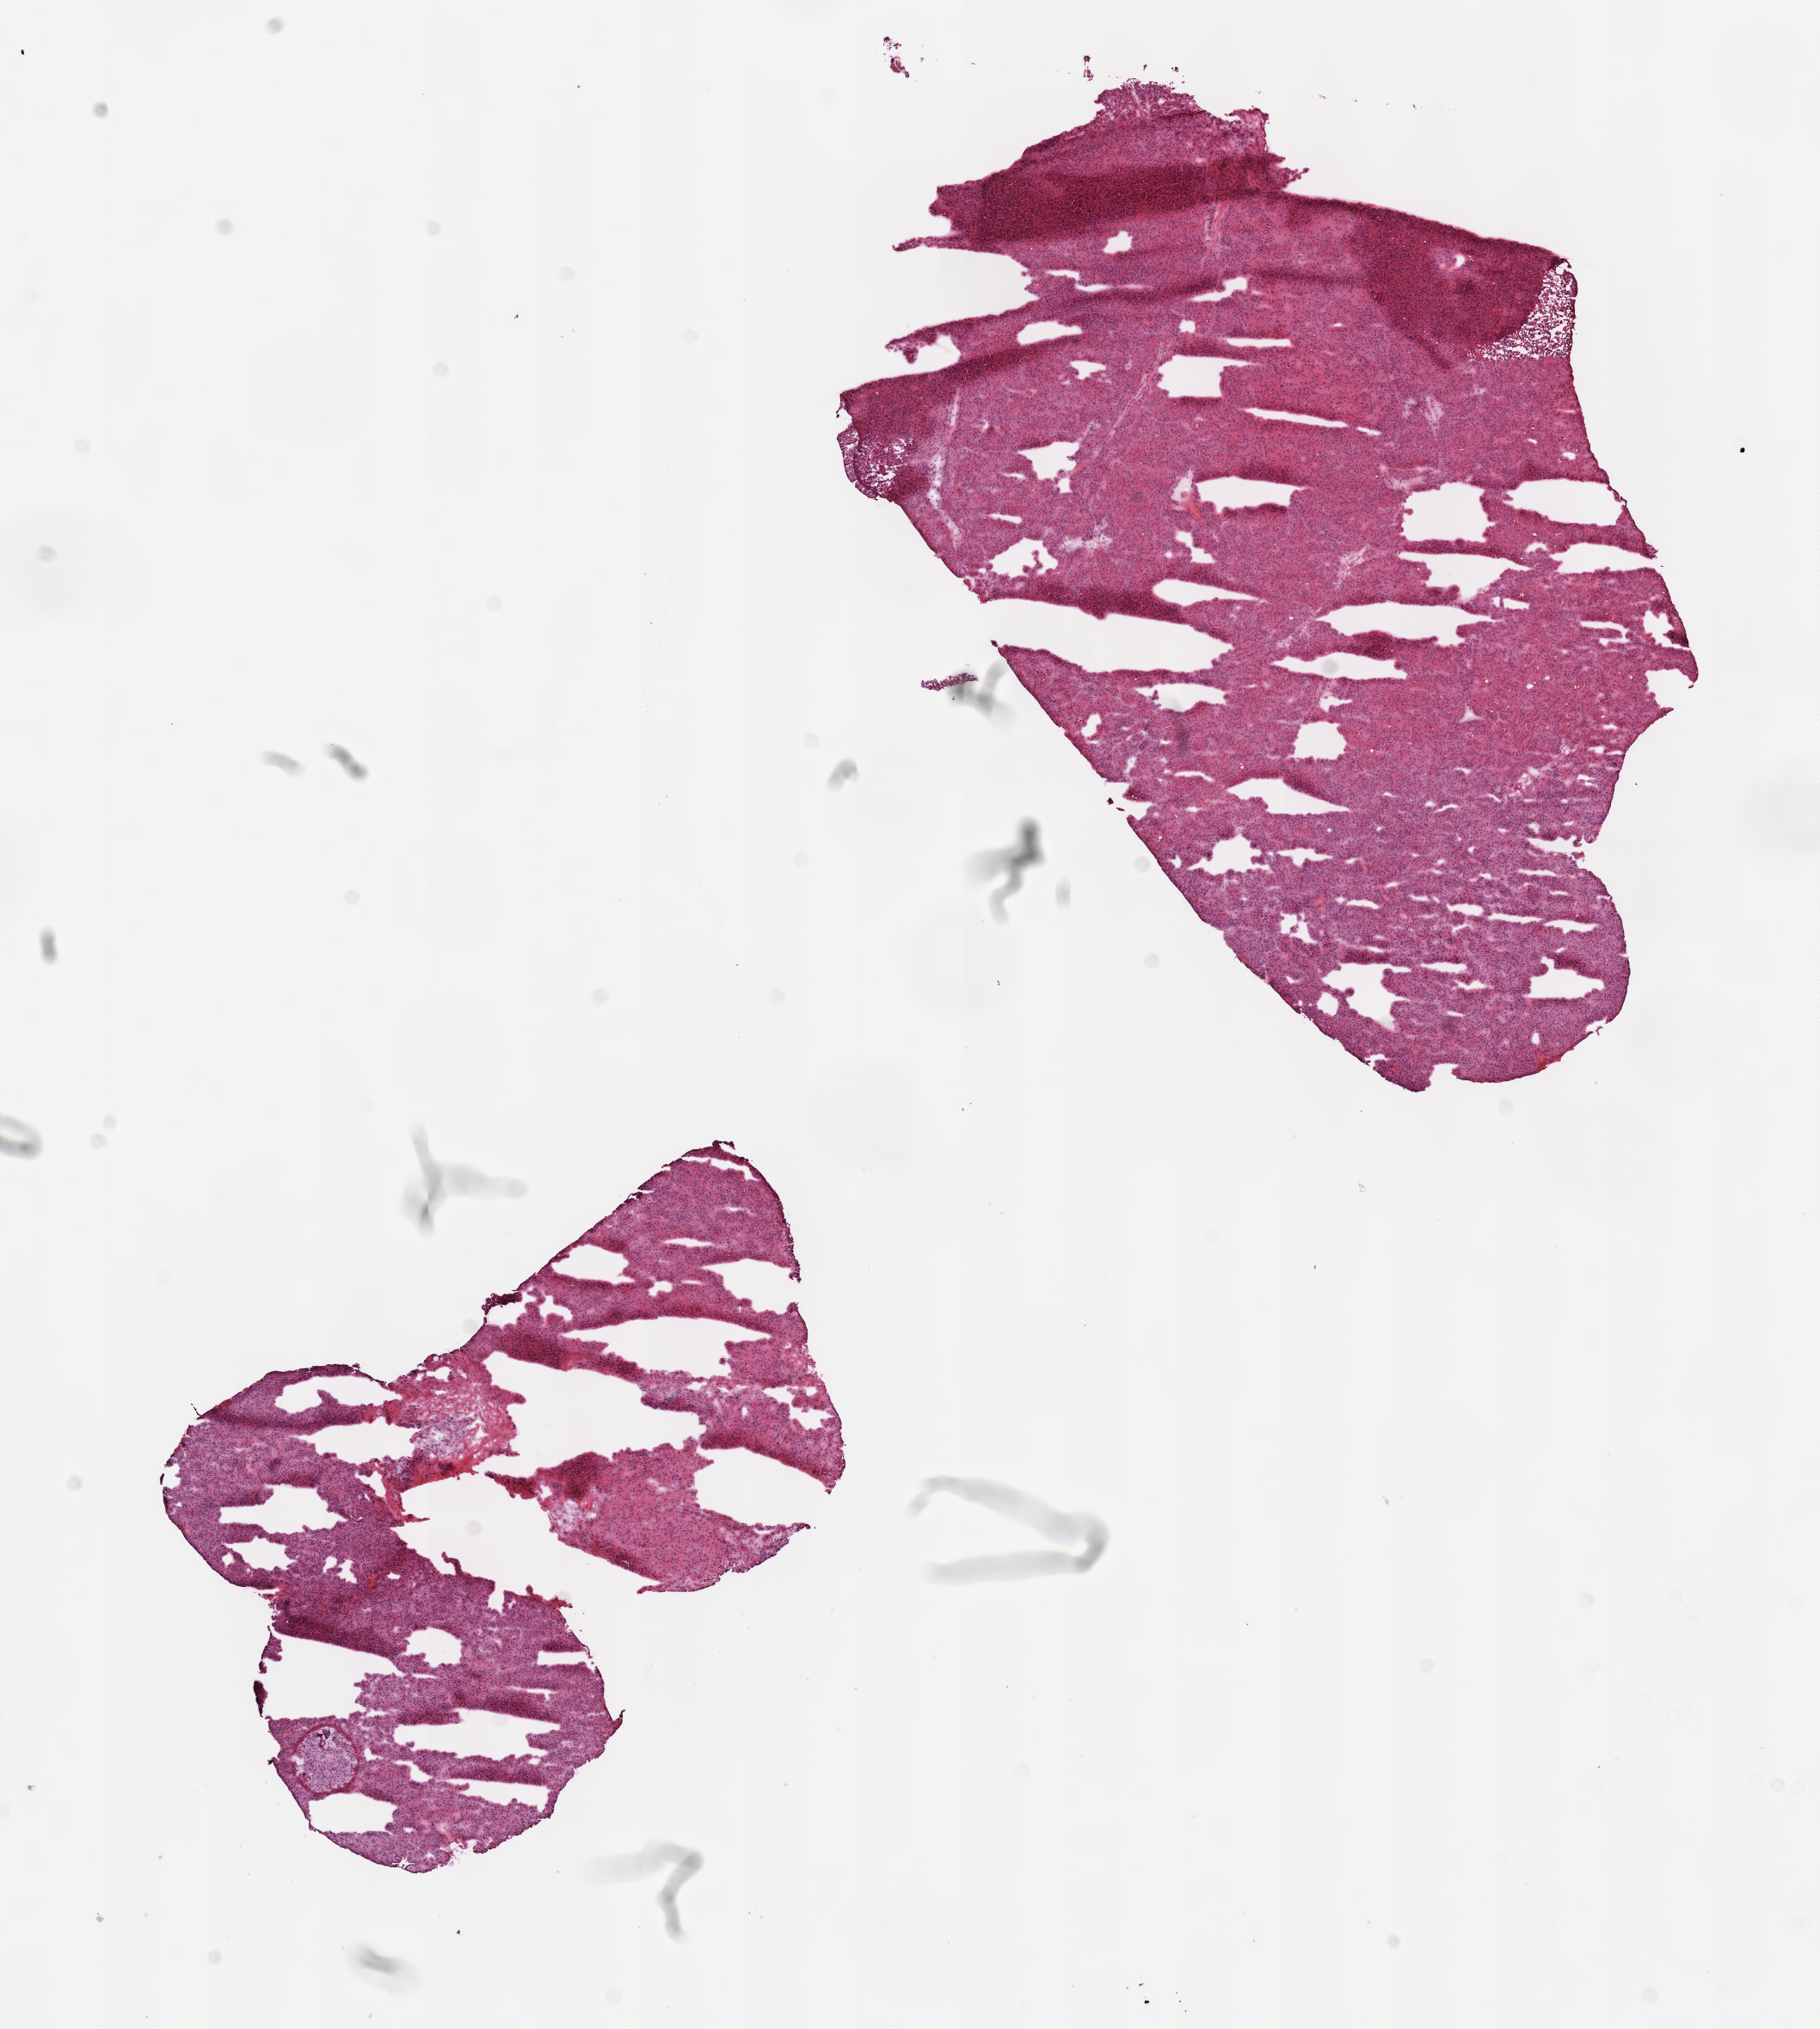
Digitized Hematoxylin and eosin (H&E) stained tissue section (whole slide), shown as a low-resolution overview of the whole scanned area (about 8.6 x 9.5 mm, slide scanned at 40x); frozen section from the top of the tissue portion; sample: primary tumour, liver. Patient: male, age at initial diagnosis 39 years. Histologic grade: G3 (poorly differentiated). Pathologist review of this section (percent, as recorded): tumour cells 90%, tumour nuclei 95%, normal cells 0%, stromal cells 10%, necrosis 0%. Inflammatory infiltration, as recorded: lymphocyte infiltration 0%, monocyte infiltration 0%, neutrophil infiltration 0%.
- AJCC pathologic stage: I
- histologic diagnosis: Hepatocellular carcinoma, NOS